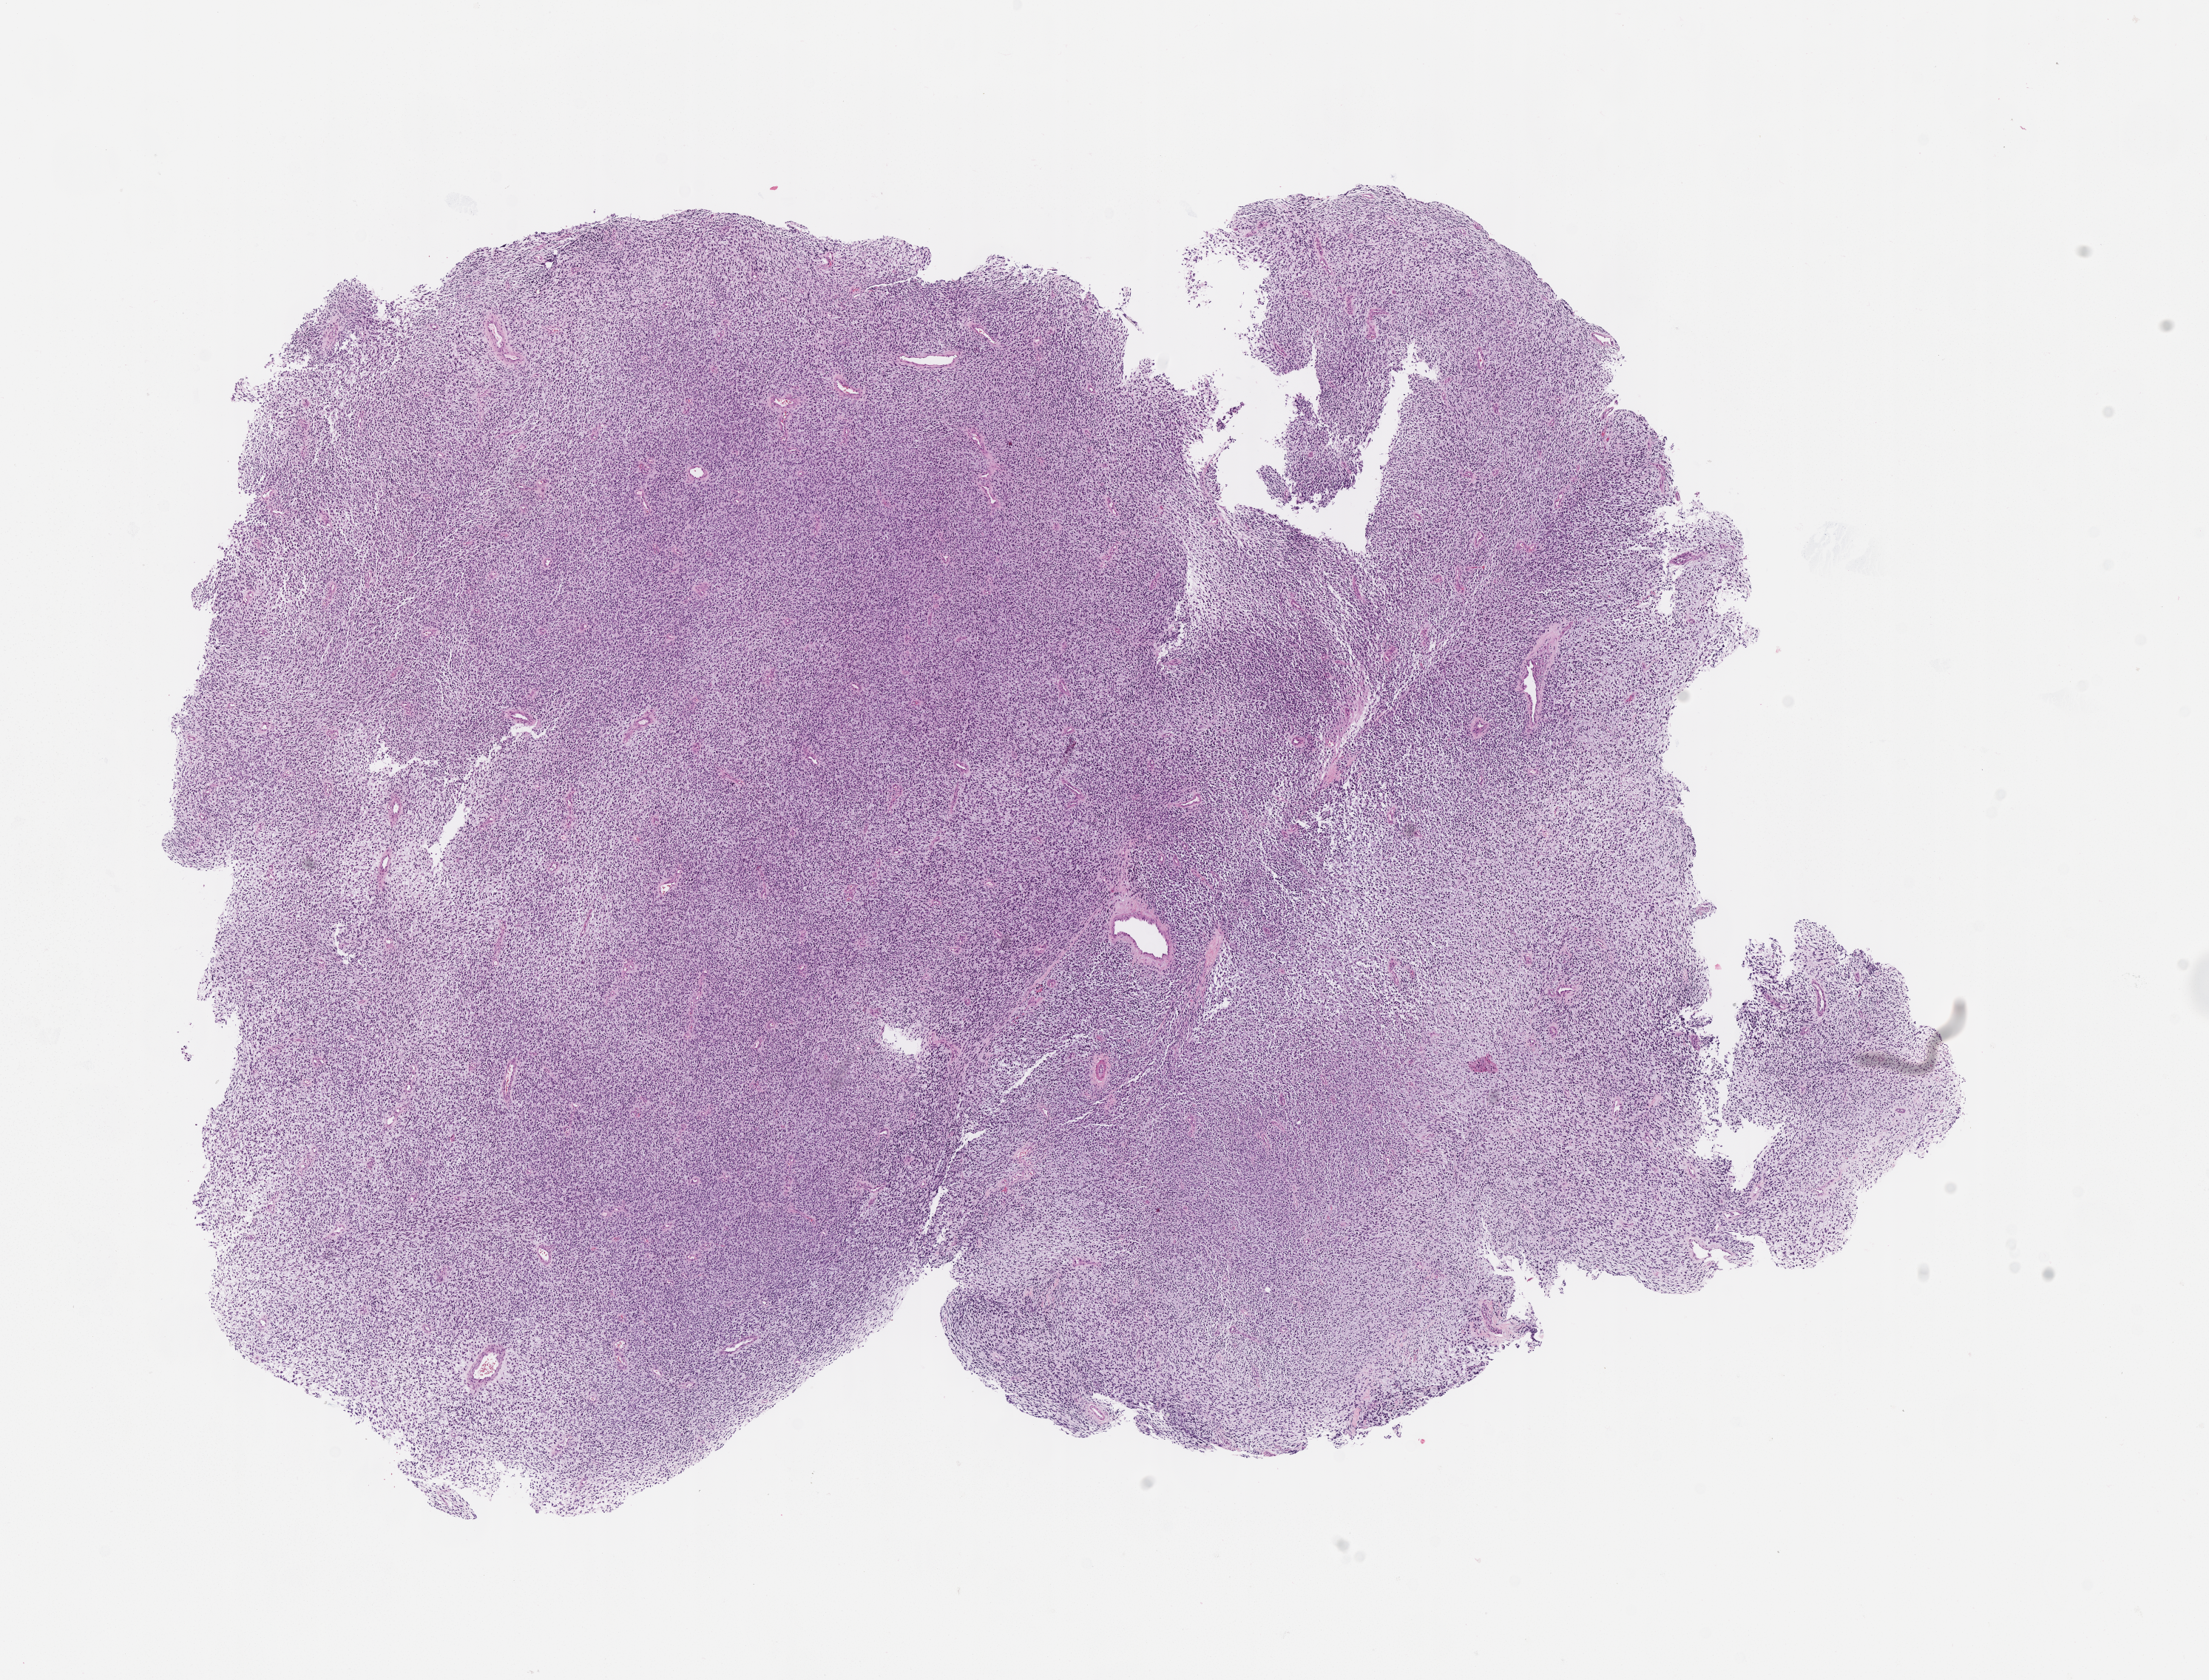
Haematoxylin and eosin whole-slide image of tumor tissue — a low-resolution overview of the entire scanned area, about 12.1 x 9.2 mm, formalin-fixed paraffin-embedded section, sample anatomic site: orbit, left. Patient: female, age 5.5 years at diagnosis.
Stage (as recorded): 1. Diagnosis: rhabdomyosarcoma; histological classification: embryonal rhabdomyosarcoma. Metastatic status at presentation (as recorded): non-metastatic (unconfirmed).